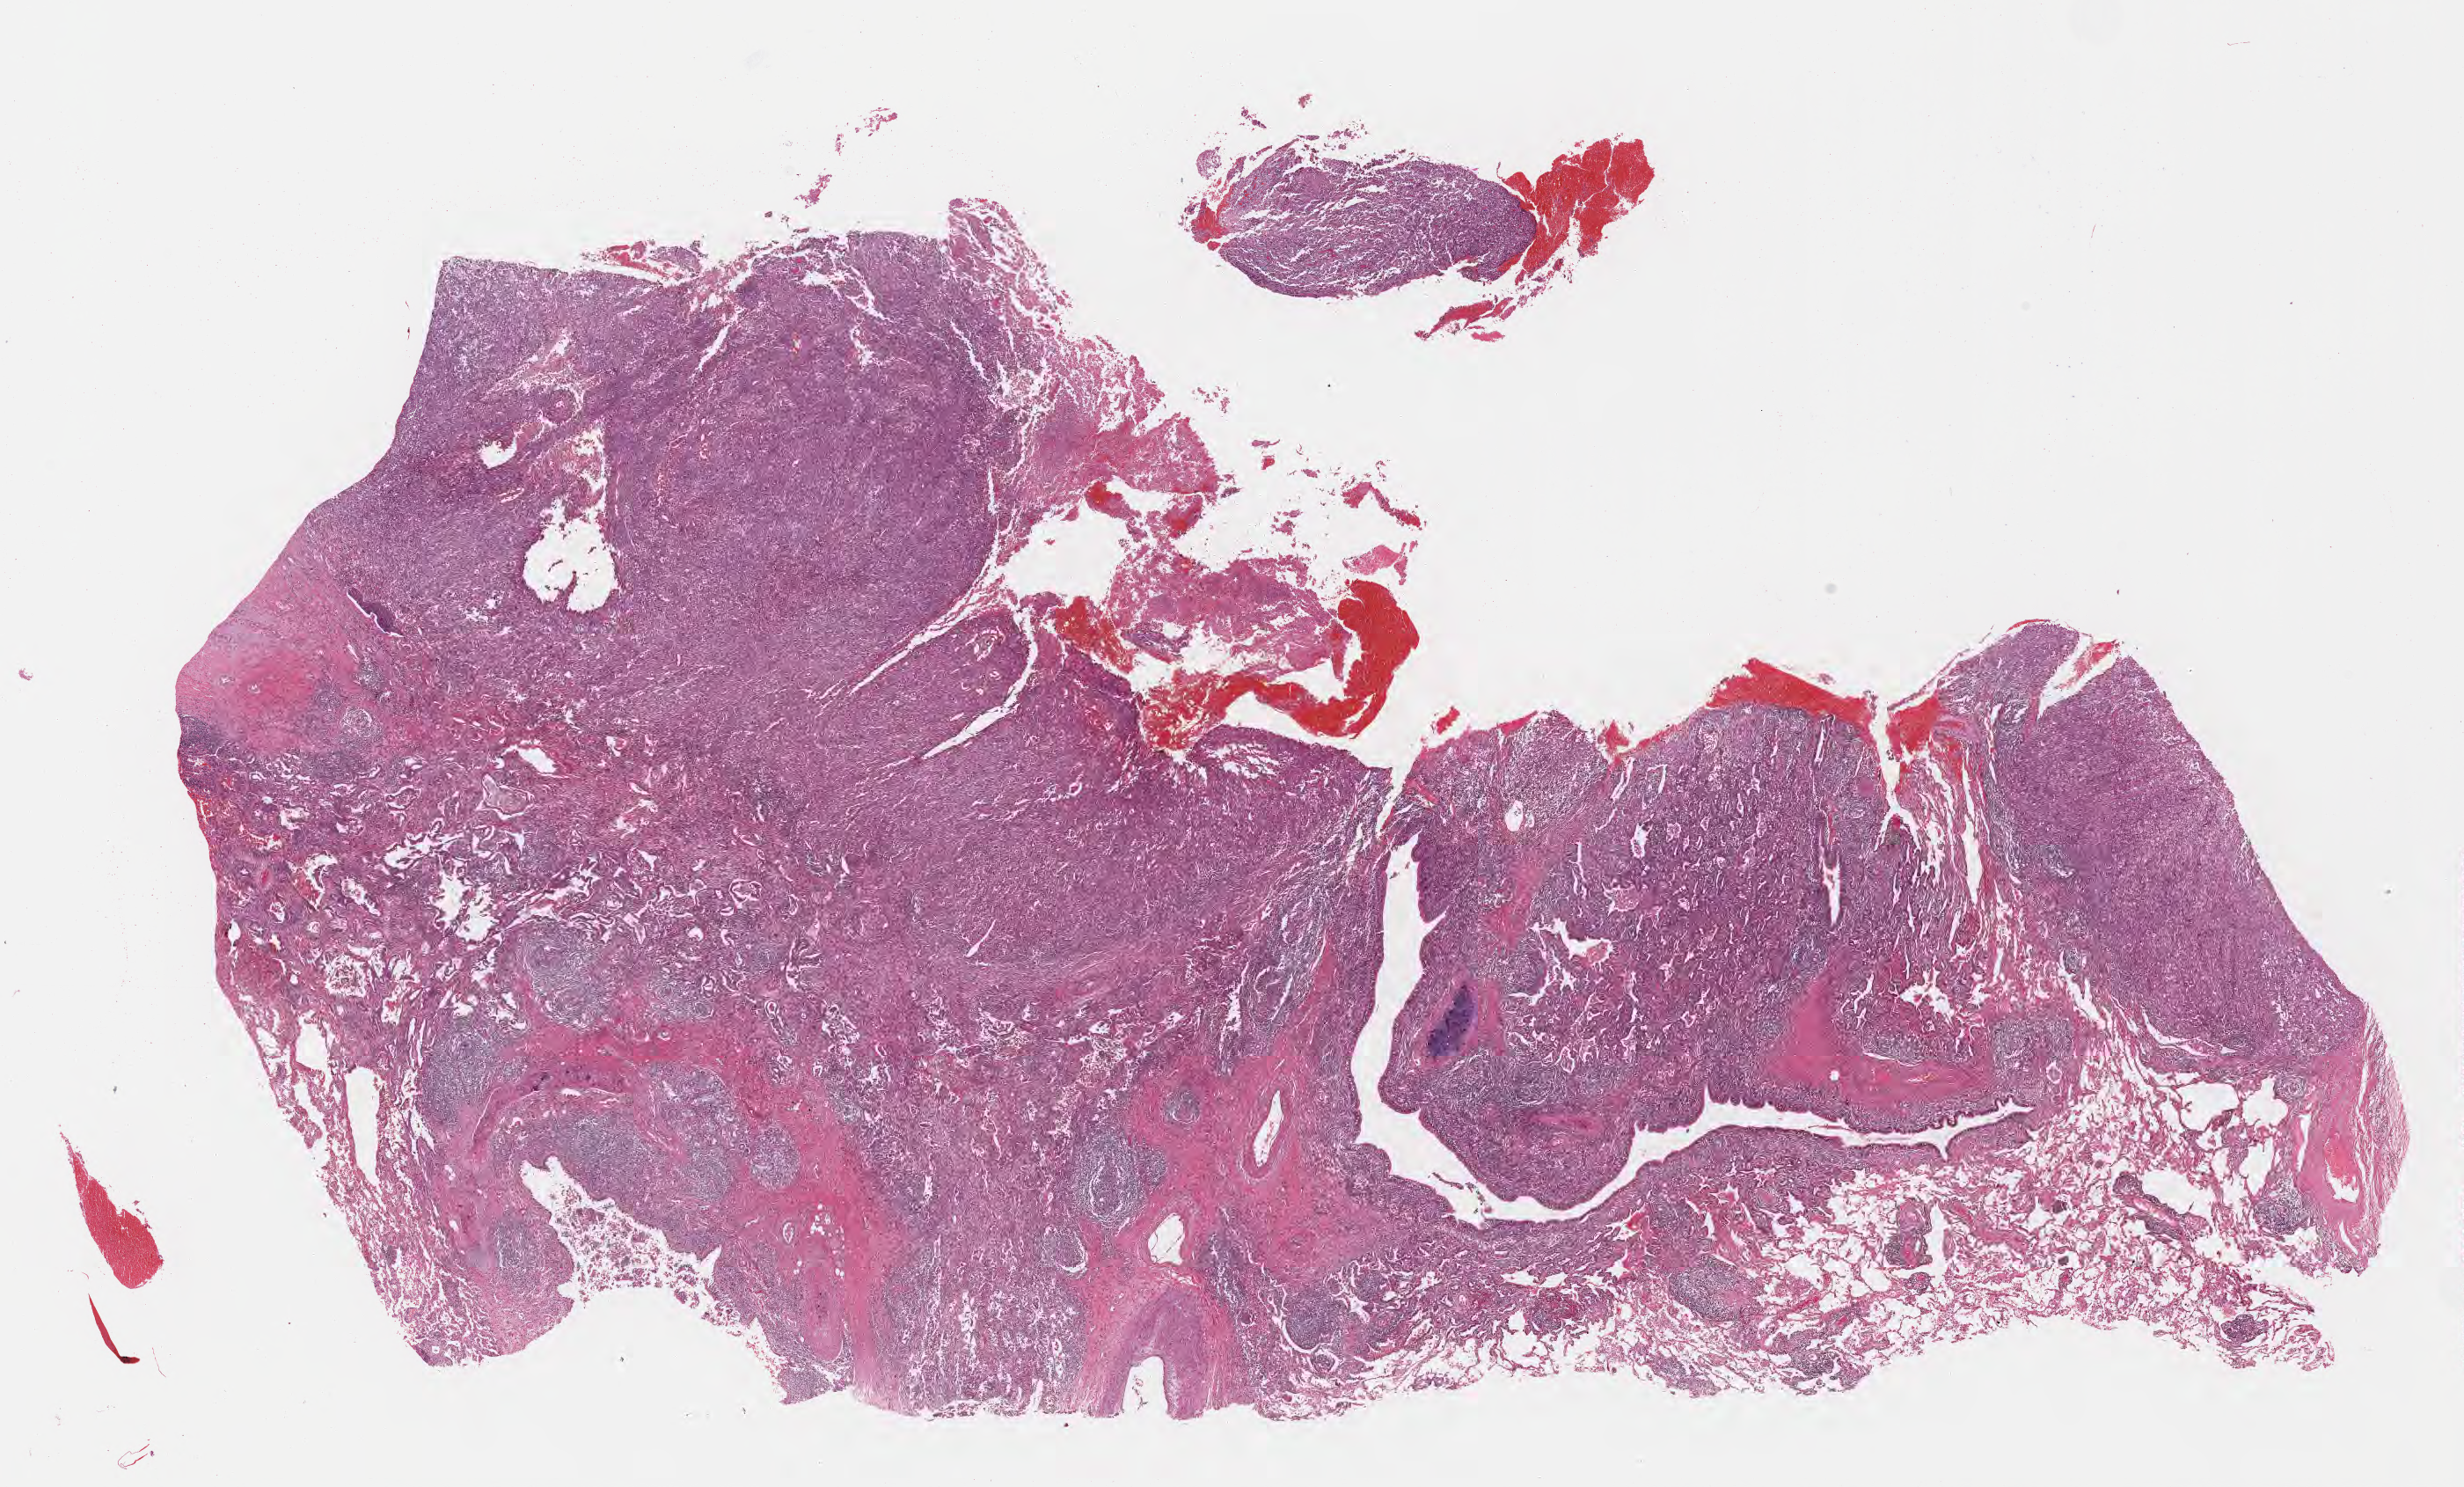
Whole-slide image, haematoxylin and eosin stain, shown as a low-resolution overview of the whole scanned area (about 22.6 x 13.7 mm), FFPE section, primary tumor, anatomic site: lower lobe of left lung. Patient: female, 79 years old. Composition of this section per pathologist review: tumor cells 90%, tumor nuclei 70%, stromal cells 0%, necrosis 0%, normal cells 10%. Infiltration values recorded for this section: lymphocyte infiltration 0%, monocyte infiltration 0%, neutrophil infiltration 0%.
* section: top of the tissue portion
* histologic diagnosis: Adenocarcinoma, NOS
* AJCC pathologic stage: Stage IIIA